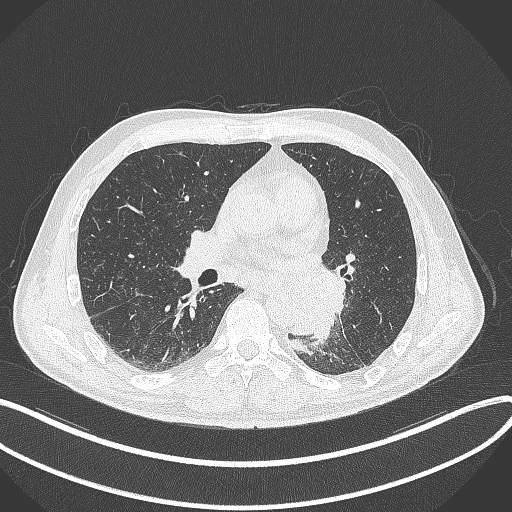
Chest CT, one axial slice; slice 171 of 329 in the series (ordered by position); lung window (W 1500 / L -600 HU); 1 mm slice thickness; 512 × 512 image matrix, field of view 400 × 400 mm. Male patient, age 59 years. From the clinical record (not read from this slice): clinical TNM (as recorded): T2a N2 M0.
Outlined on this slice (bounding box drawn by a radiologist):
- lung tumour (recorded histology: squamous cell carcinoma): bounding box (x1, y1, x2, y2) in pixels: (288, 264, 349, 339)